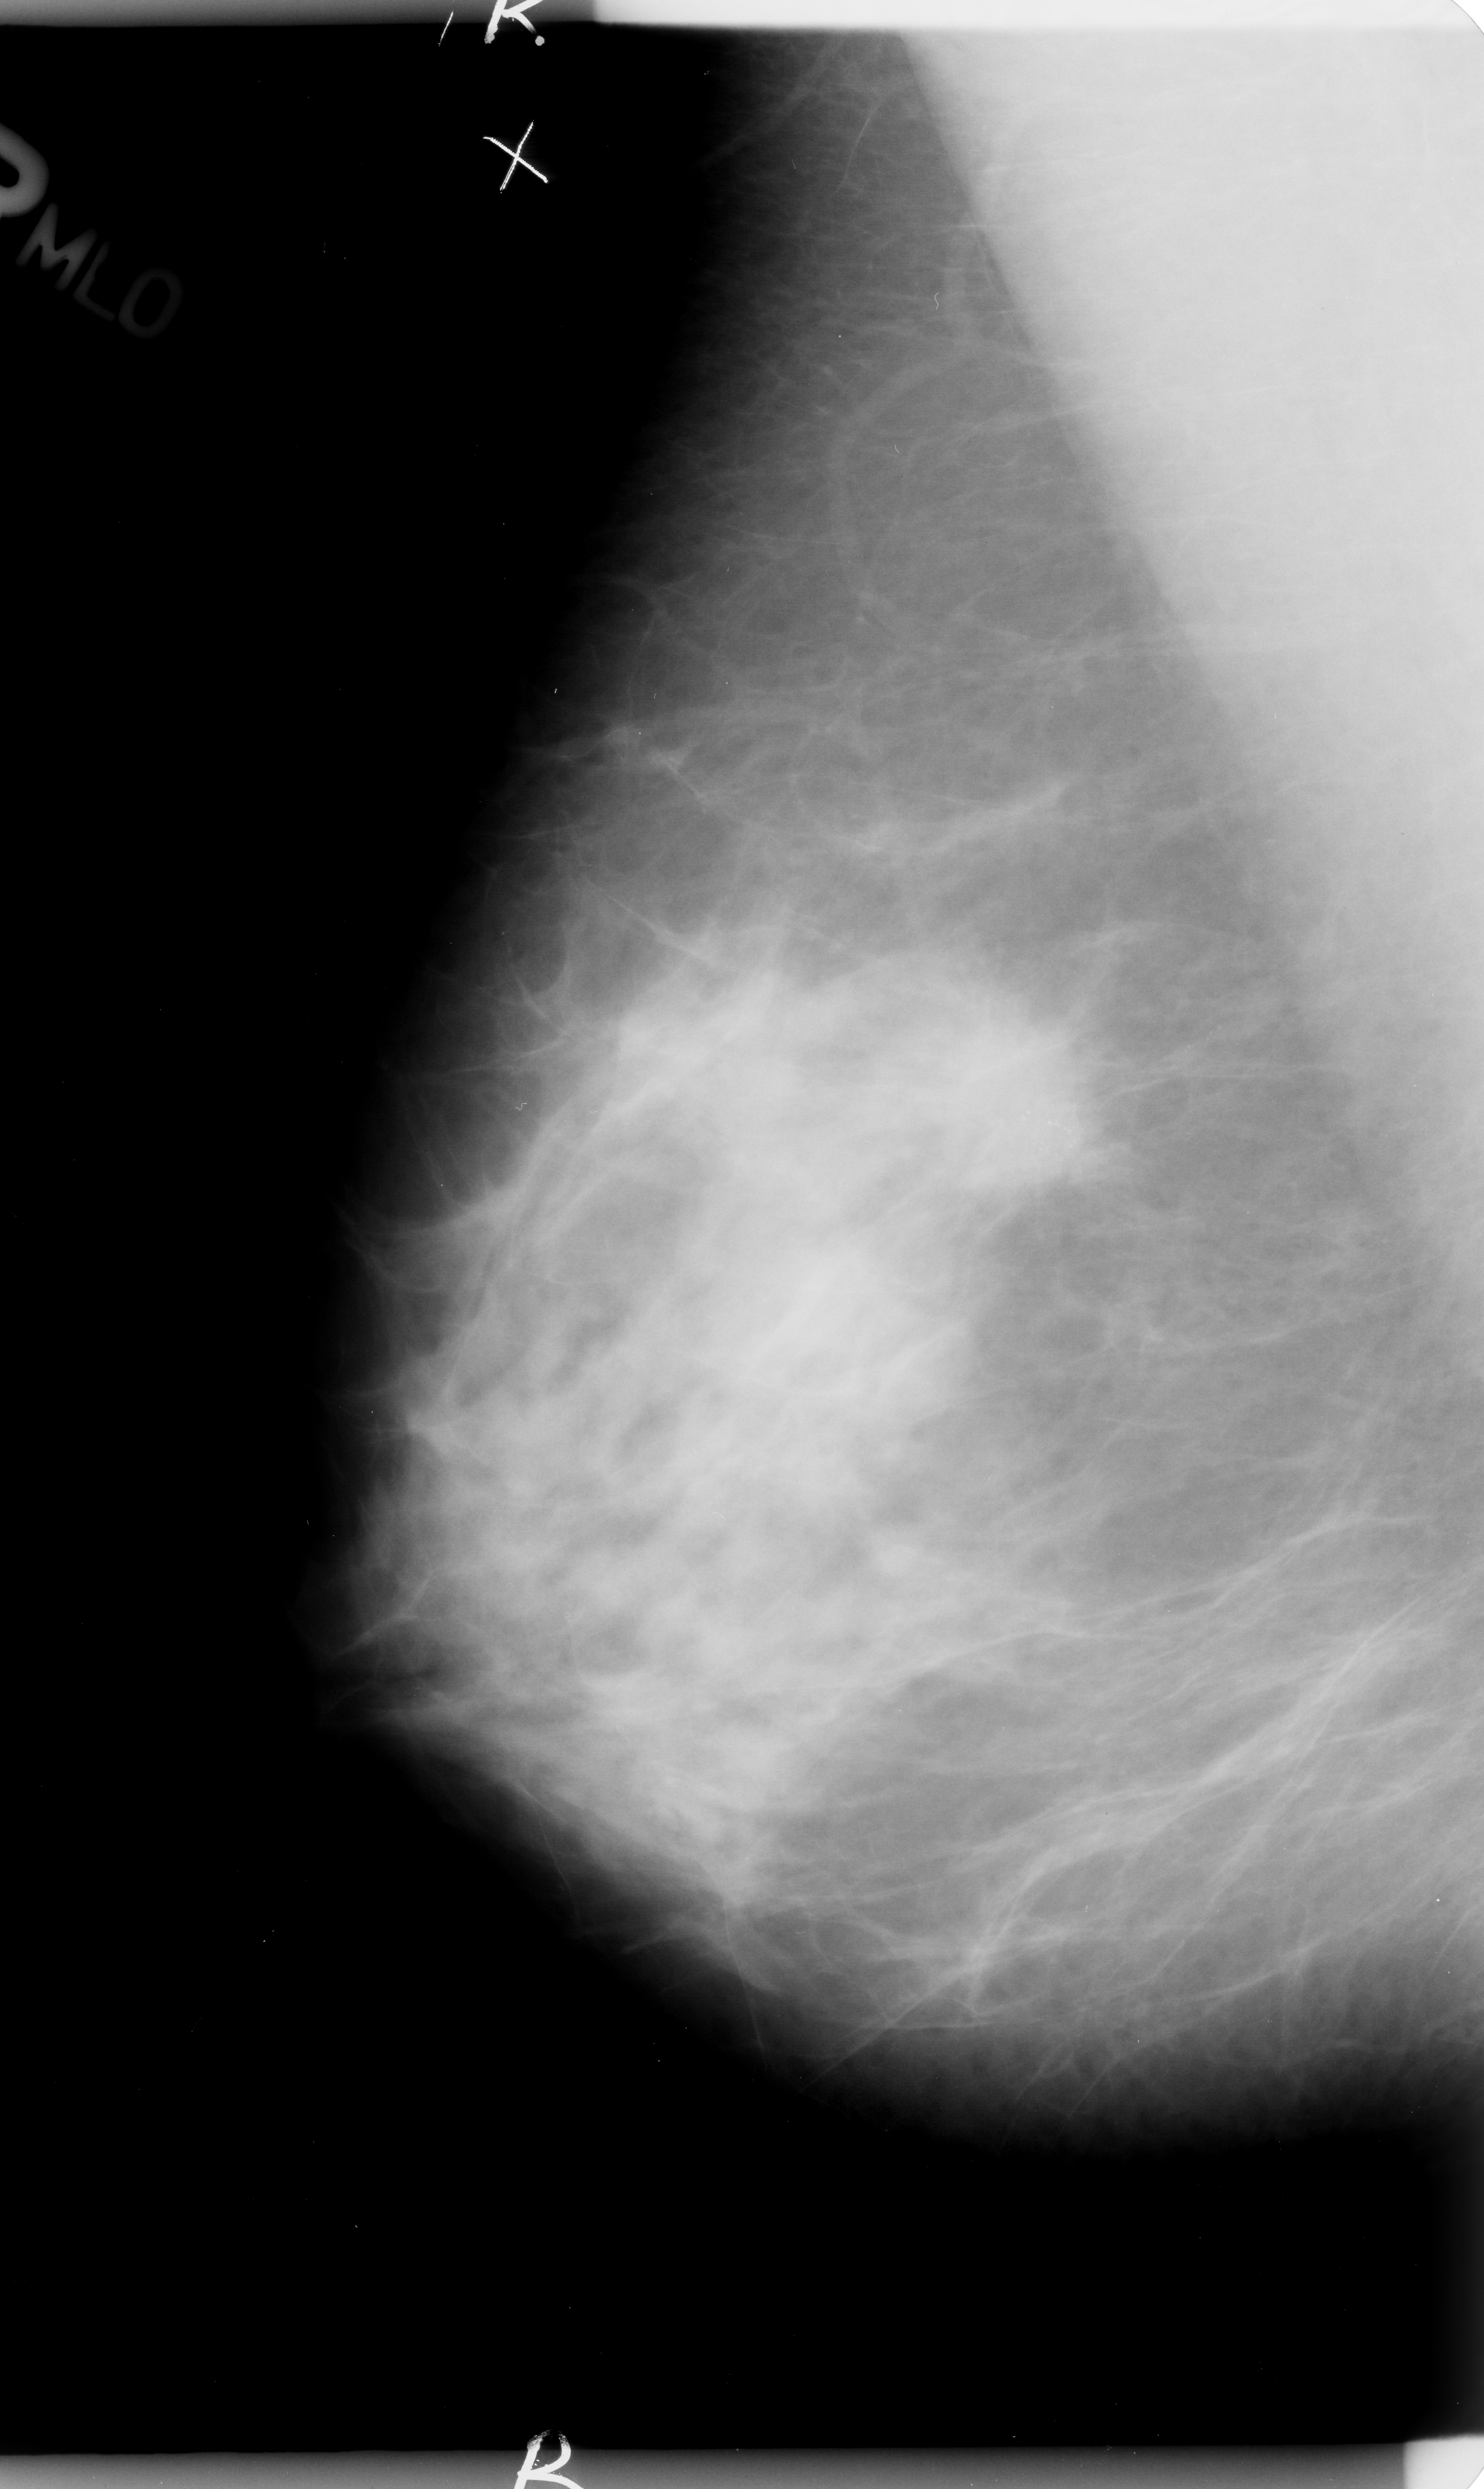
Digitized screen-film mammogram, right breast, mediolateral oblique (MLO) view, breast composition: heterogeneously dense (BI-RADS density category 3 of 4).
Marked findings (only marked abnormalities are described; nothing is implied about the rest of the image): calcifications, morphology pleomorphic, distribution clustered / linear; BI-RADS assessment category 5; subtlety rating 4 on a 1 (subtle) to 5 (obvious) scale; pathology (as recorded): malignant.